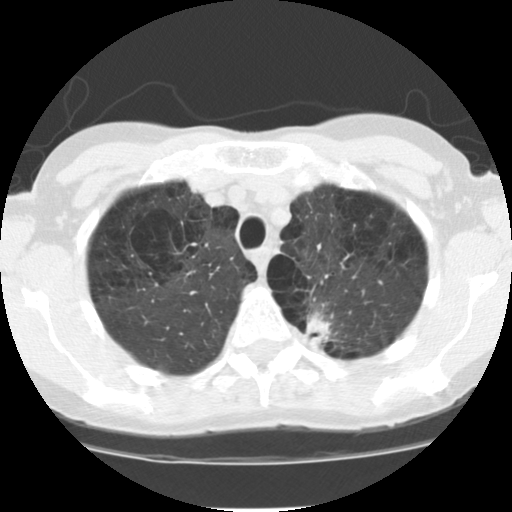
Chest CT (low-dose screening protocol), one axial image, baseline screening round, lung window (W 1500 / L -600 HU), 2.5 mm slice thickness, 120 kVp, slice 23 of 116 in the series. Female participant, aged 61 years at enrolment. Current smoker at enrolment.
• Expert-annotated lung lesion, bounding box <287,304,346,360> (left, top, right, bottom; pixels).
• The screening reader recorded 4 non-calcified nodules or masses ≥4 mm on this exam; which of them this box marks is not recorded.